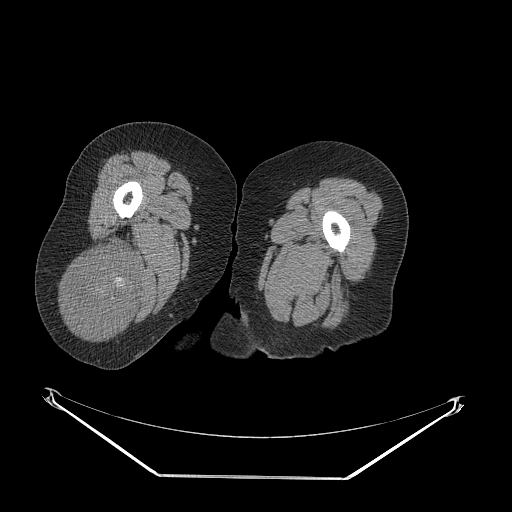
CT of an extremity soft-tissue mass (from a PET/CT study), one axial slice. Slice 36 of 257 in the series (ordered by position). 140 kVp. Soft-tissue window (W 400 / L 40 HU). 3.75 mm slice thickness. 512 × 512 image matrix, field of view 500 × 500 mm. Female patient. From the clinical record (not read from this slice): histological type: synovial sarcoma; grade: intermediate; site of the primary tumour: right buttock.
Structures marked on this image (expert contour drawn on MRI and transferred to this co-registered scan by the dataset authors):
- gross tumour volume including surrounding oedema: bounding box [x1, y1, x2, y2] px = [64, 238, 142, 336]
- gross tumour volume (mass): [64, 247, 142, 336]